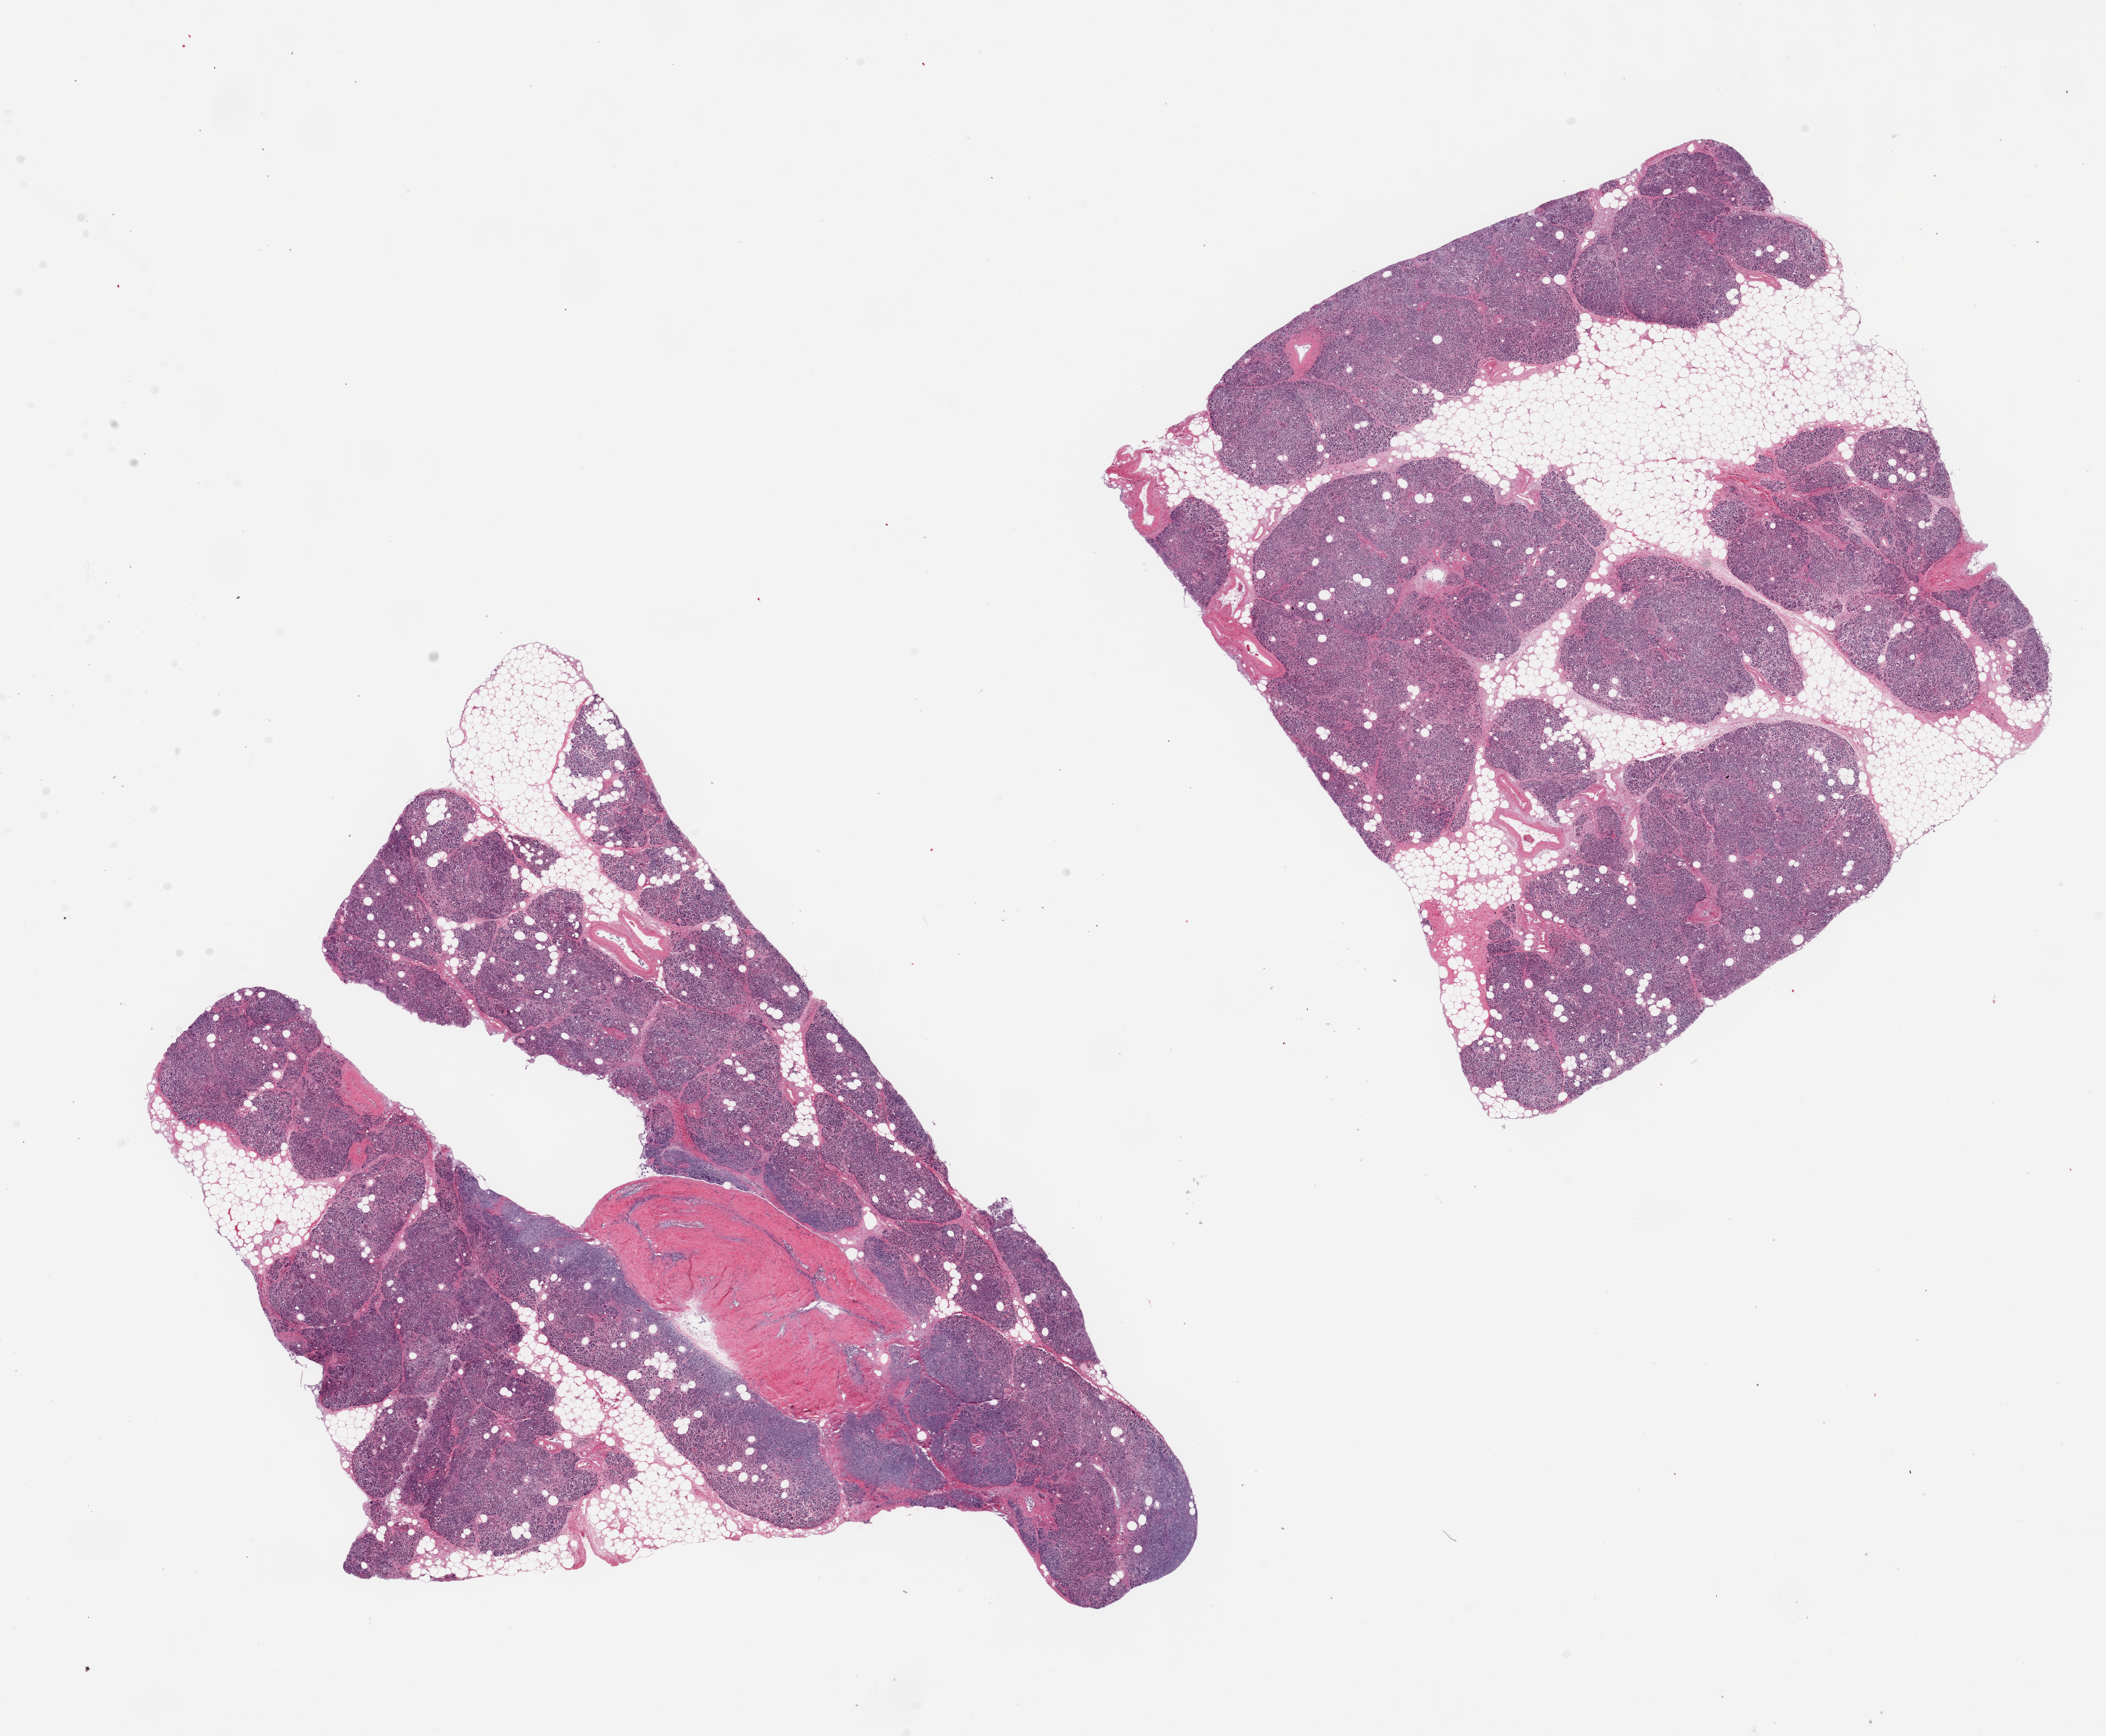
Whole-slide image, haematoxylin and eosin stain, brightfield, shown as a low-resolution overview of the whole scanned area (about 23.6 x 19.5 mm). PAXgene-fixed paraffin-embedded (PFPE) section. Sampled site (target tissue): pancreas. Donor tissue sample.
• review note (as recorded): 2 pieces; severe autolysis; 20% & 40% intralobular fat